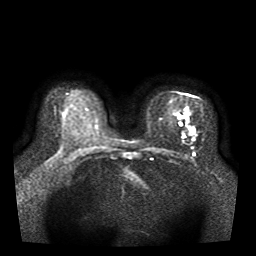
Breast MRI, one axial slice; slice 23 of 41 in the series (ordered by position); diffusion-weighted series; image 2 of 4 stored at this slice position (different b-values; order by instance number); 1.5 T; 5 mm slice thickness; 256 × 256 image matrix. Female patient.
Structures marked on this image (outlined manually by an expert reader):
- tumour on diffusion-weighted imaging: bounding box <192,128,195,133> (left, top, right, bottom; pixels)